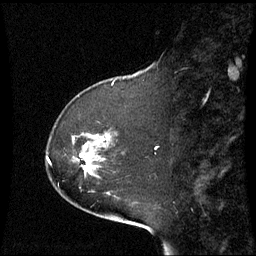
Breast MRI (dynamic contrast-enhanced), one sagittal slice; position 19 of 60 along the scan axis; dynamic contrast-enhanced series, image 2 of 3 at this slice position (ordered by acquisition); 1.5 T; TE 4.2 ms, TR 8.9 ms; 2.4 mm slice thickness; 256 × 256 image matrix. Female patient, age 51 years. From the clinical record (not read from this slice): setting: breast cancer imaged before/during neoadjuvant chemotherapy; receptor status: HR-positive, HER2-negative.
Annotated regions visible in this slice (semi-automatically segmented with operator editing):
- analysis volume of interest (the breast-tissue region the enhancement analysis was run in; not a lesion): bounding box [x1, y1, x2, y2] px = [72, 133, 111, 194]
- tumour enhancement mask (voxels above the 70 % enhancement threshold inside the analysis volume of interest): [82, 154, 88, 171]